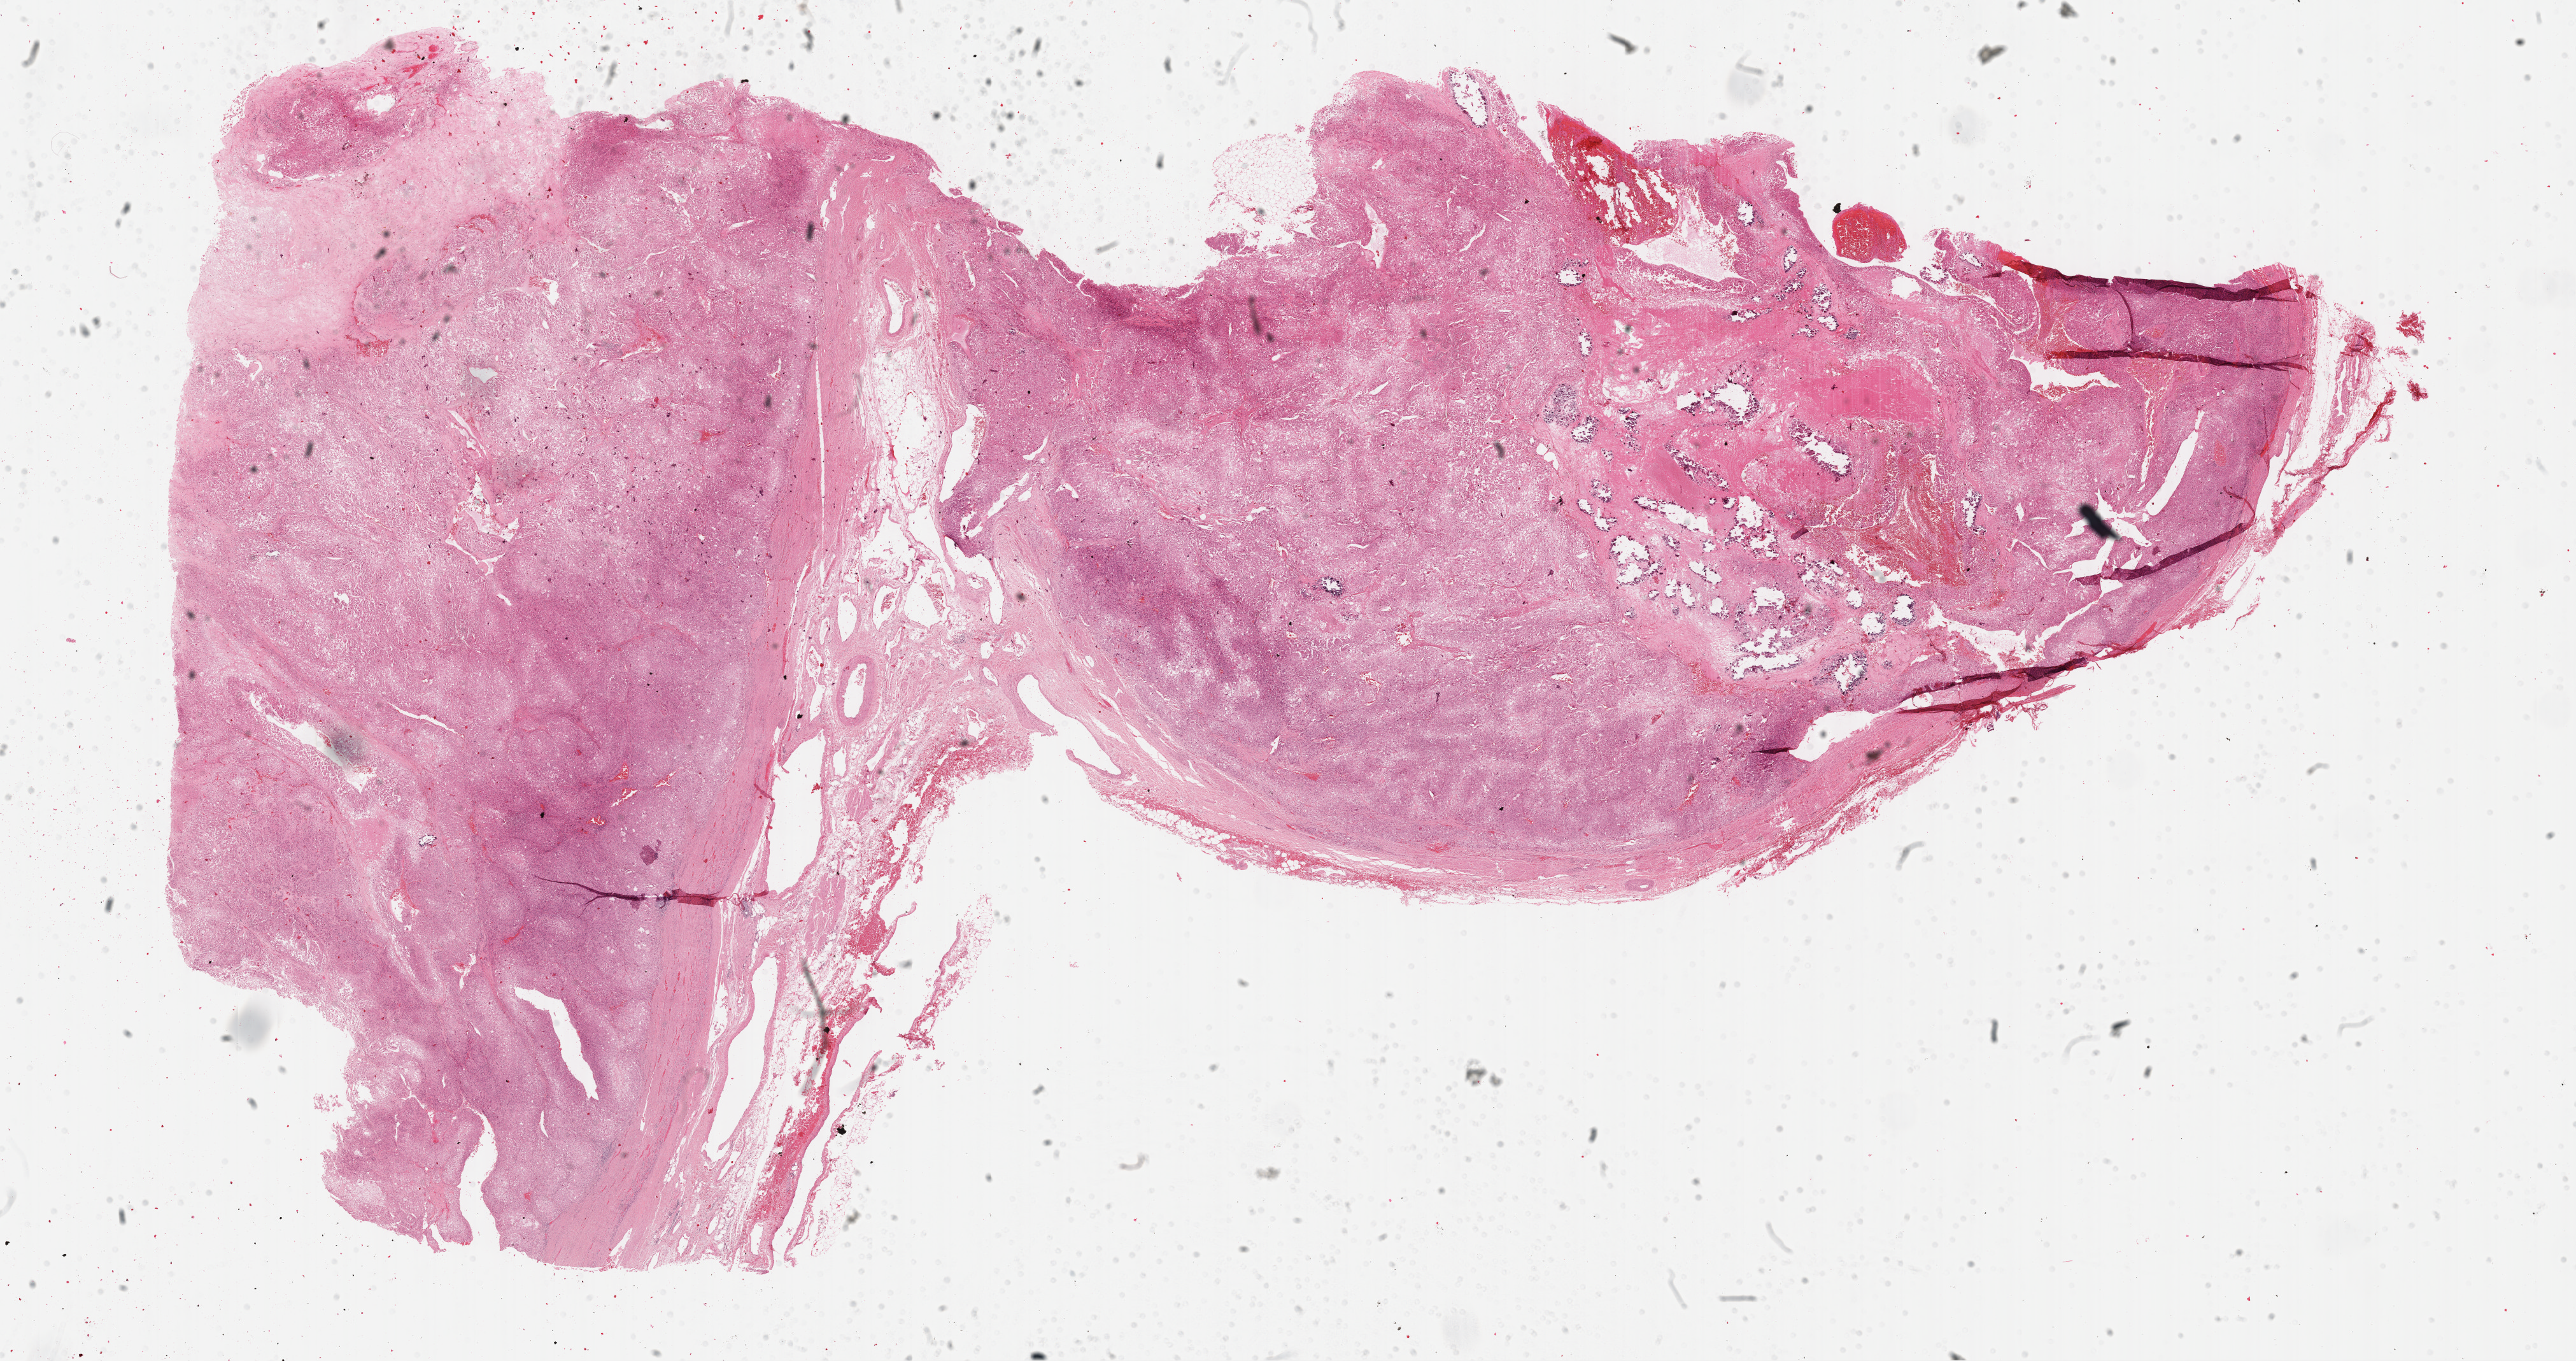
Hematoxylin and eosin (H&E) stained whole-slide image, a low-resolution overview of the entire scanned area, about 32.7 x 17.3 mm (slide scanned at 40x), formalin-fixed paraffin-embedded (FFPE) diagnostic section, sample: primary tumour, adrenal cortex. Patient: male, age at initial diagnosis 49 years.
Histologic diagnosis: Adrenal cortical carcinoma (cortex of adrenal gland).